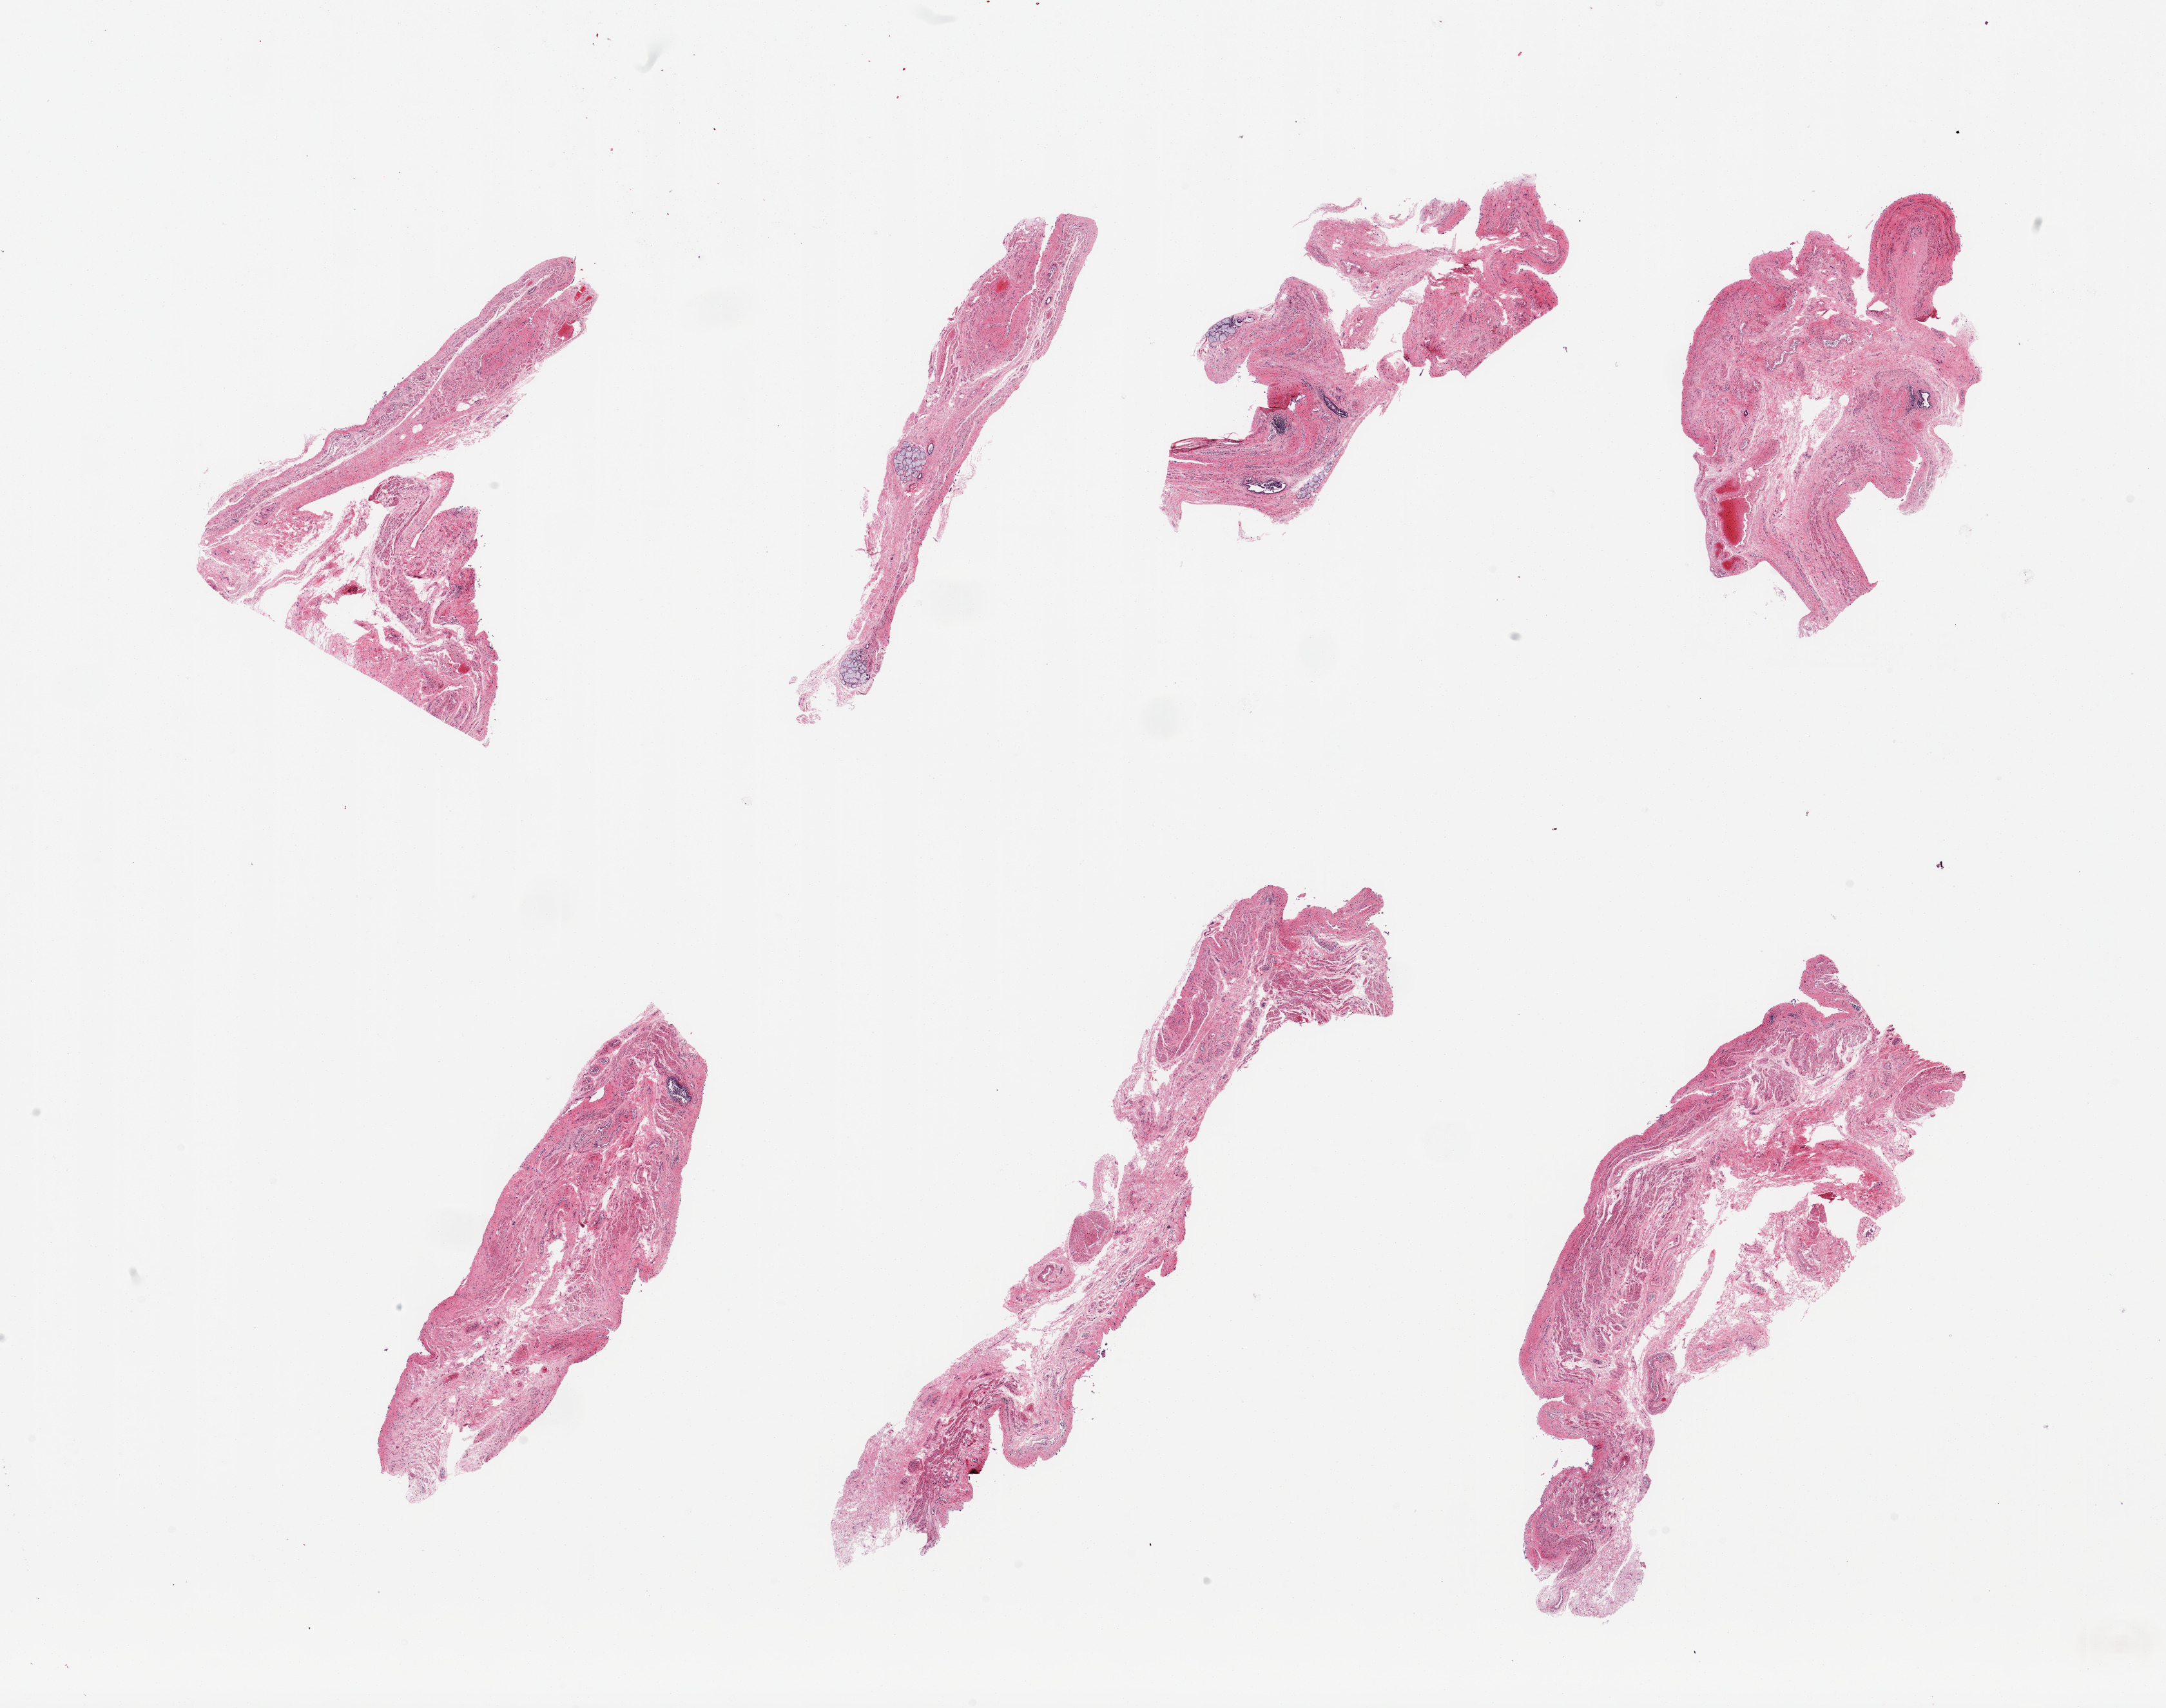
Whole-slide image, hematoxylin and eosin (H&E) stain, whole scanned area (about 26.6 x 21.0 mm) shown as a low-resolution overview, PAXgene-fixed paraffin-embedded (PFPE) section, sampled site (target tissue): esophageal mucous membrane, donor tissue sample. Donor: female.
Reviewer comment on this tissue sample: 6 pieces, squamous mucosa with advanced autolysis/sloughed; few residual submucosal mucus glands present.